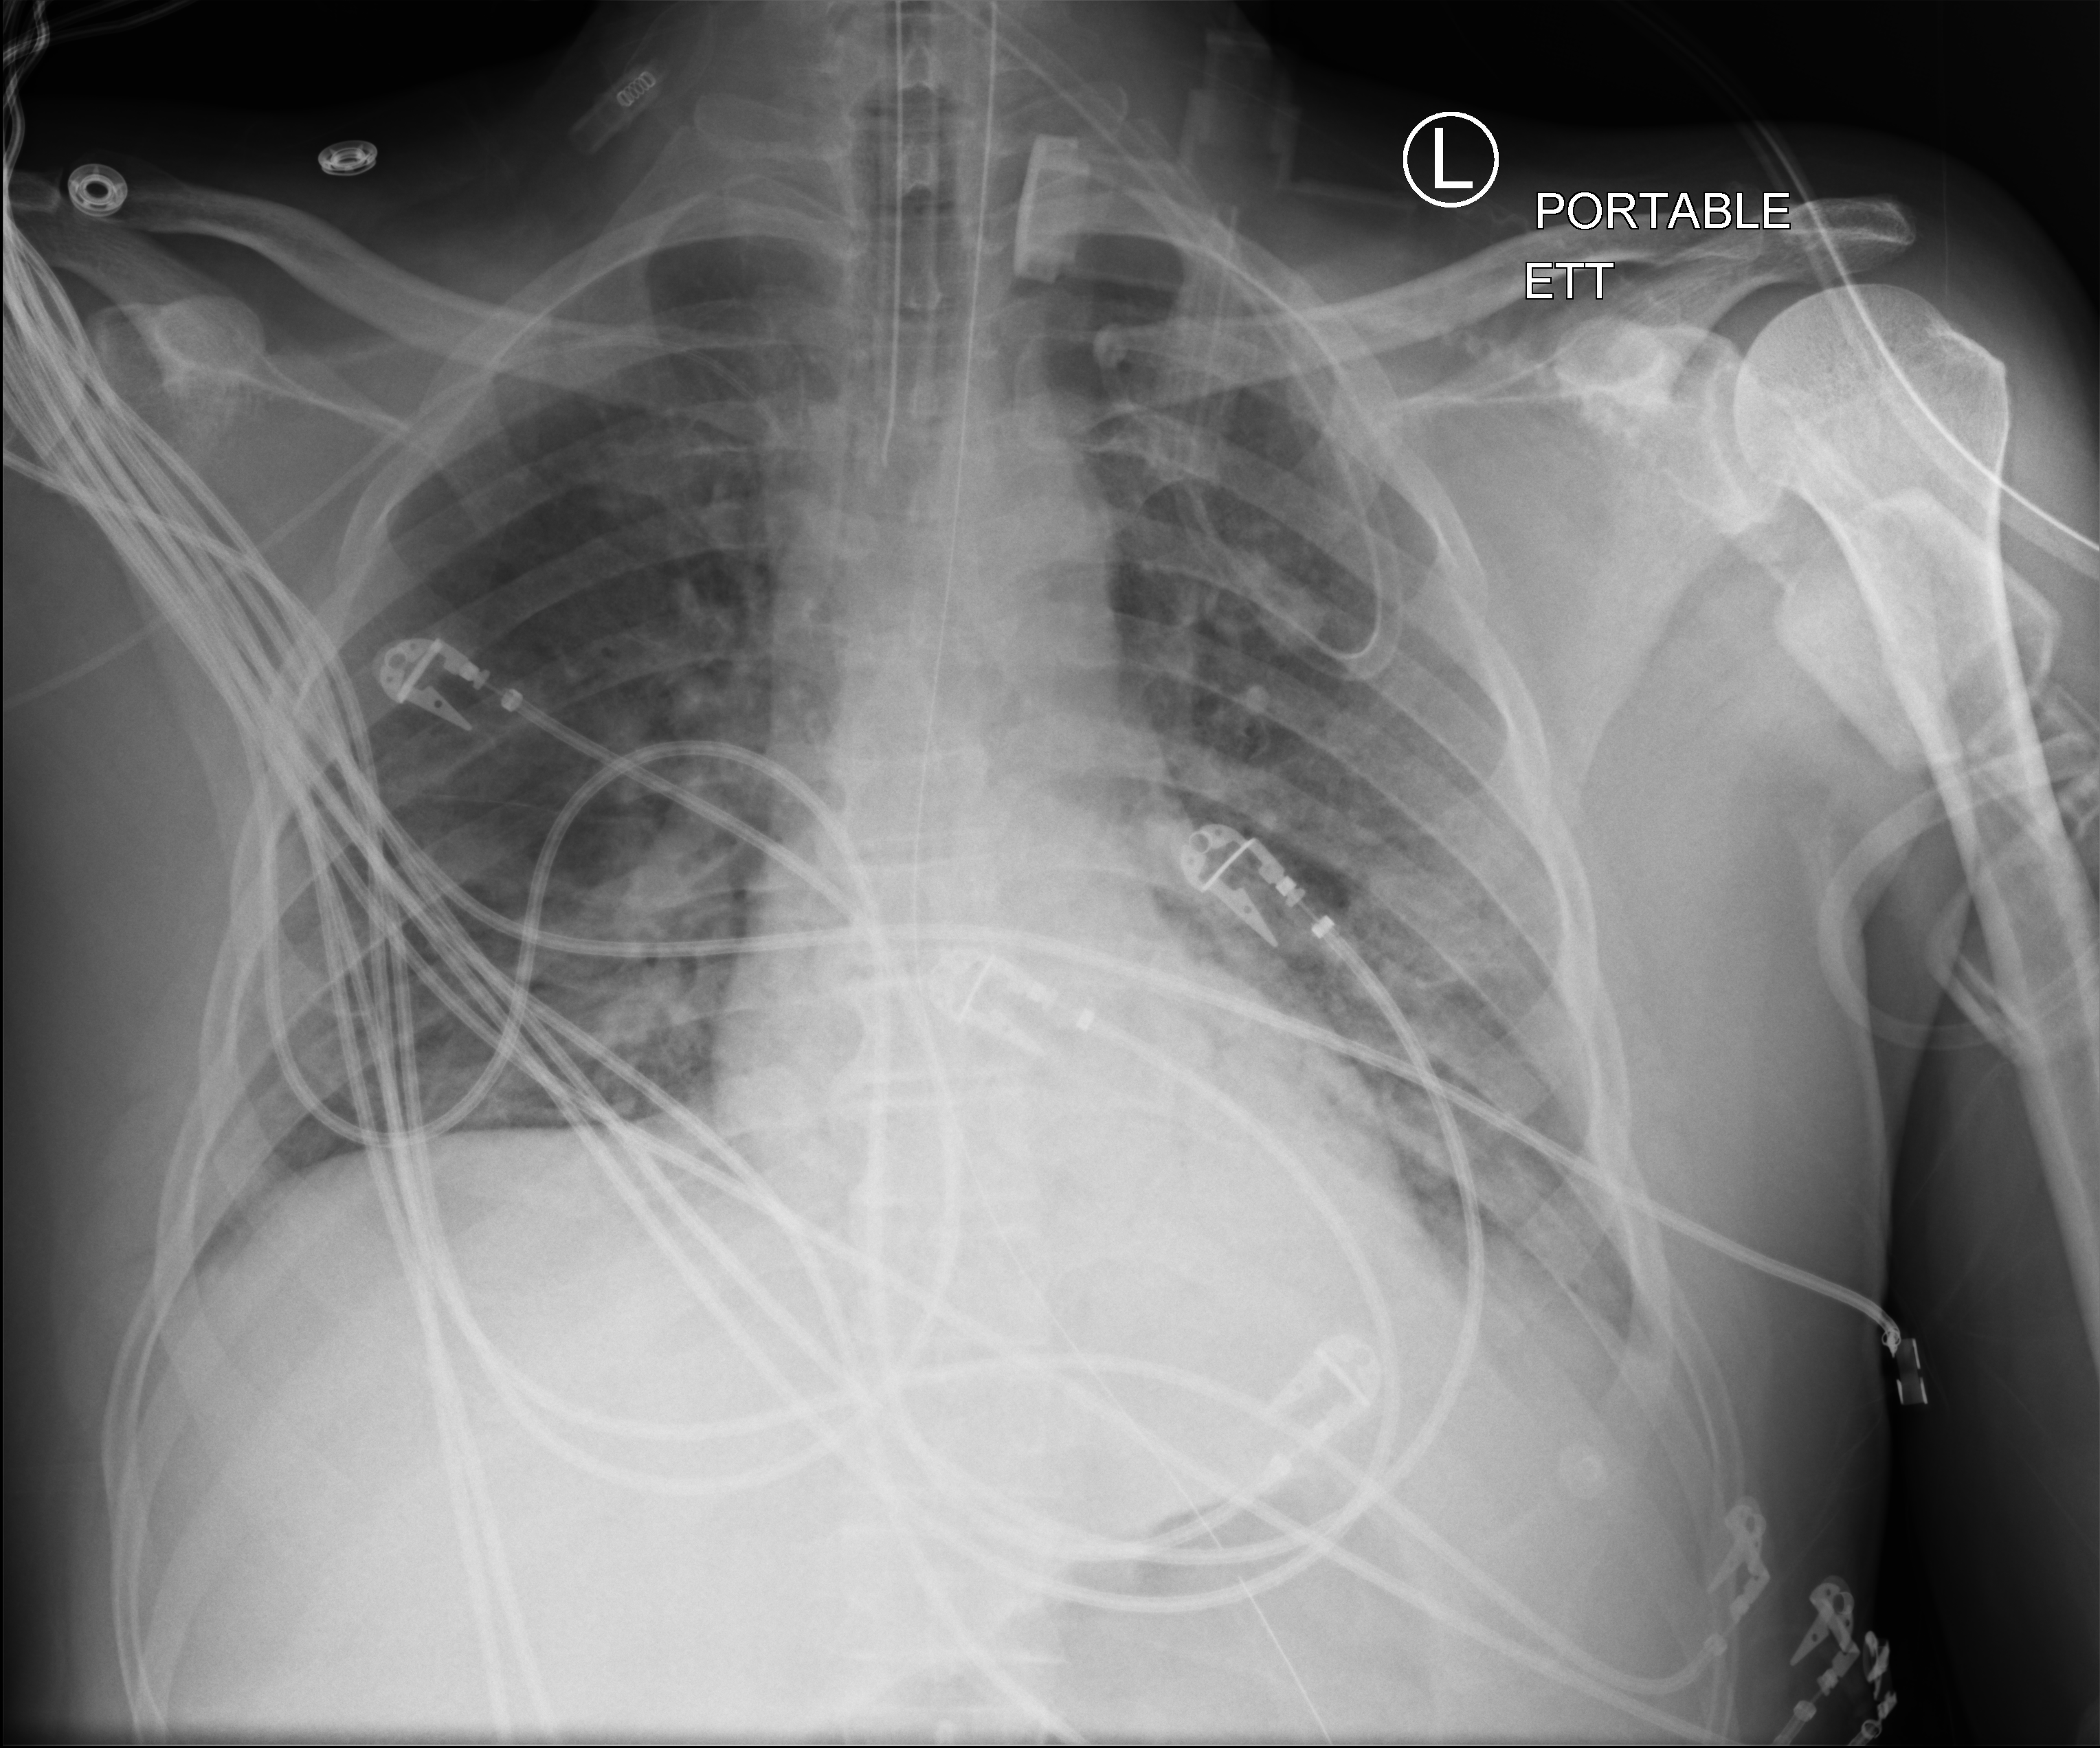
Chest X-ray (portable); anteroposterior (AP) projection. Patient hospitalised with COVID-19; male, aged 18–59 years.
Hospital-stay facts (about this admission, not read from this image; timing relative to this image not recorded):
- mechanically ventilated during this hospital stay: yes
- length of hospital stay: 83 days
- smoking status (admission record): never